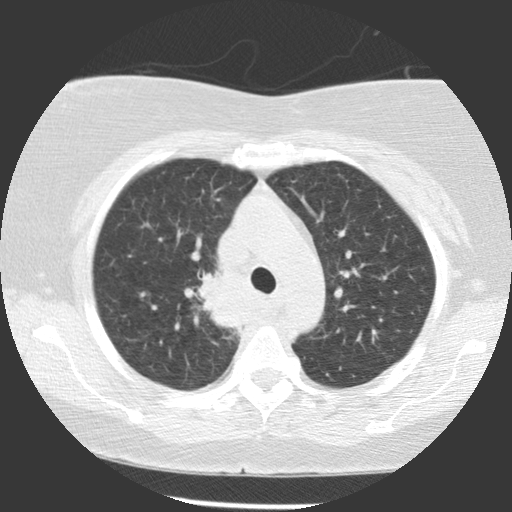
Axial slice from a low-dose chest CT screening exam, baseline screening round, lung window (W 1500 / L -600 HU), standard (soft-tissue) reconstruction kernel (STANDARD), 512 × 512 image matrix. Female participant, aged 63 years at enrolment.
Expert-annotated lung lesion, box from (x=192, y=264) to (x=253, y=325) px. Reader record for this screening exam (exam-level; its link to the box is not recorded): non-calcified nodule or mass ≥4 mm, right upper lobe, 39 × 36 mm, spiculated (stellate) margins, soft tissue attenuation. Official screen result: positive, change unspecified: nodule(s) >= 4 mm or enlarging nodule(s), mass(es), or other non-specific abnormalities suspicious for lung cancer. Lung cancer was diagnosed 72 days after this screen: non-small cell carcinoma, right upper lobe, carina, right main stem bronchus, poorly differentiated (G3), stage IIIA (AJCC 6th edition), 66 mm at pathology.